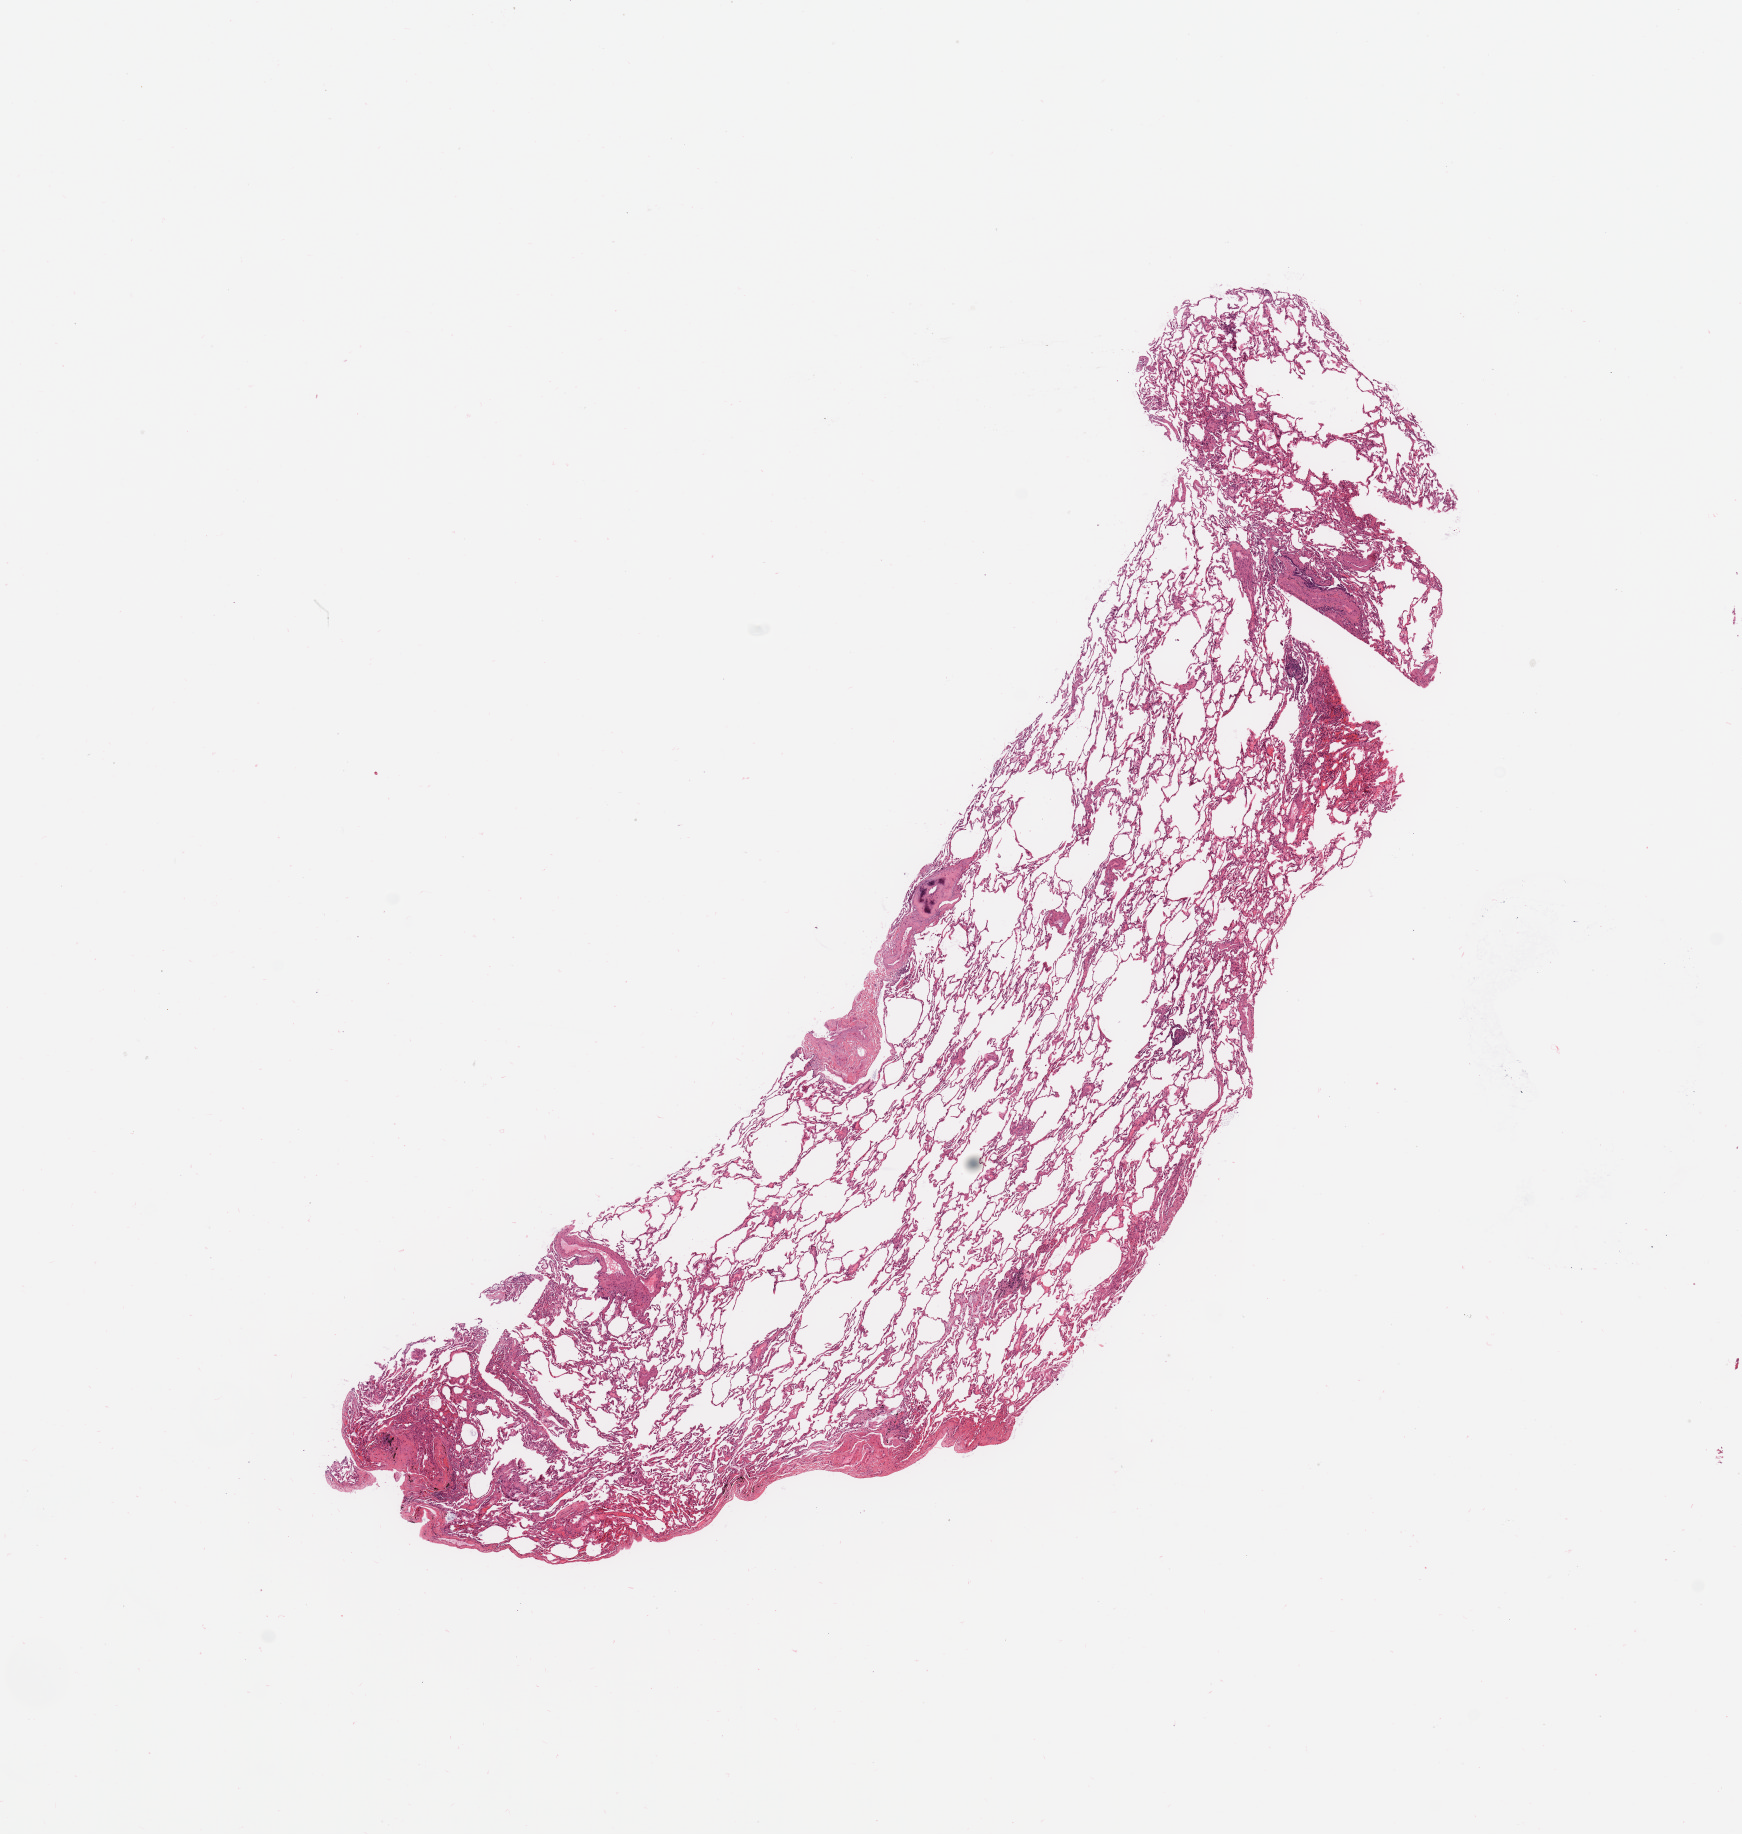
Whole-slide histology image, H&E, a low-resolution overview of the entire scanned area, about 13.8 x 14.5 mm (from a 20x scan). Normal (non-tumour) tissue sample, sampled site: lung. Patient: female, age 70 years.
This section: normal (non-tumour) tissue from the same patient. Patient diagnosis: Adenocarcinoma, NOS.